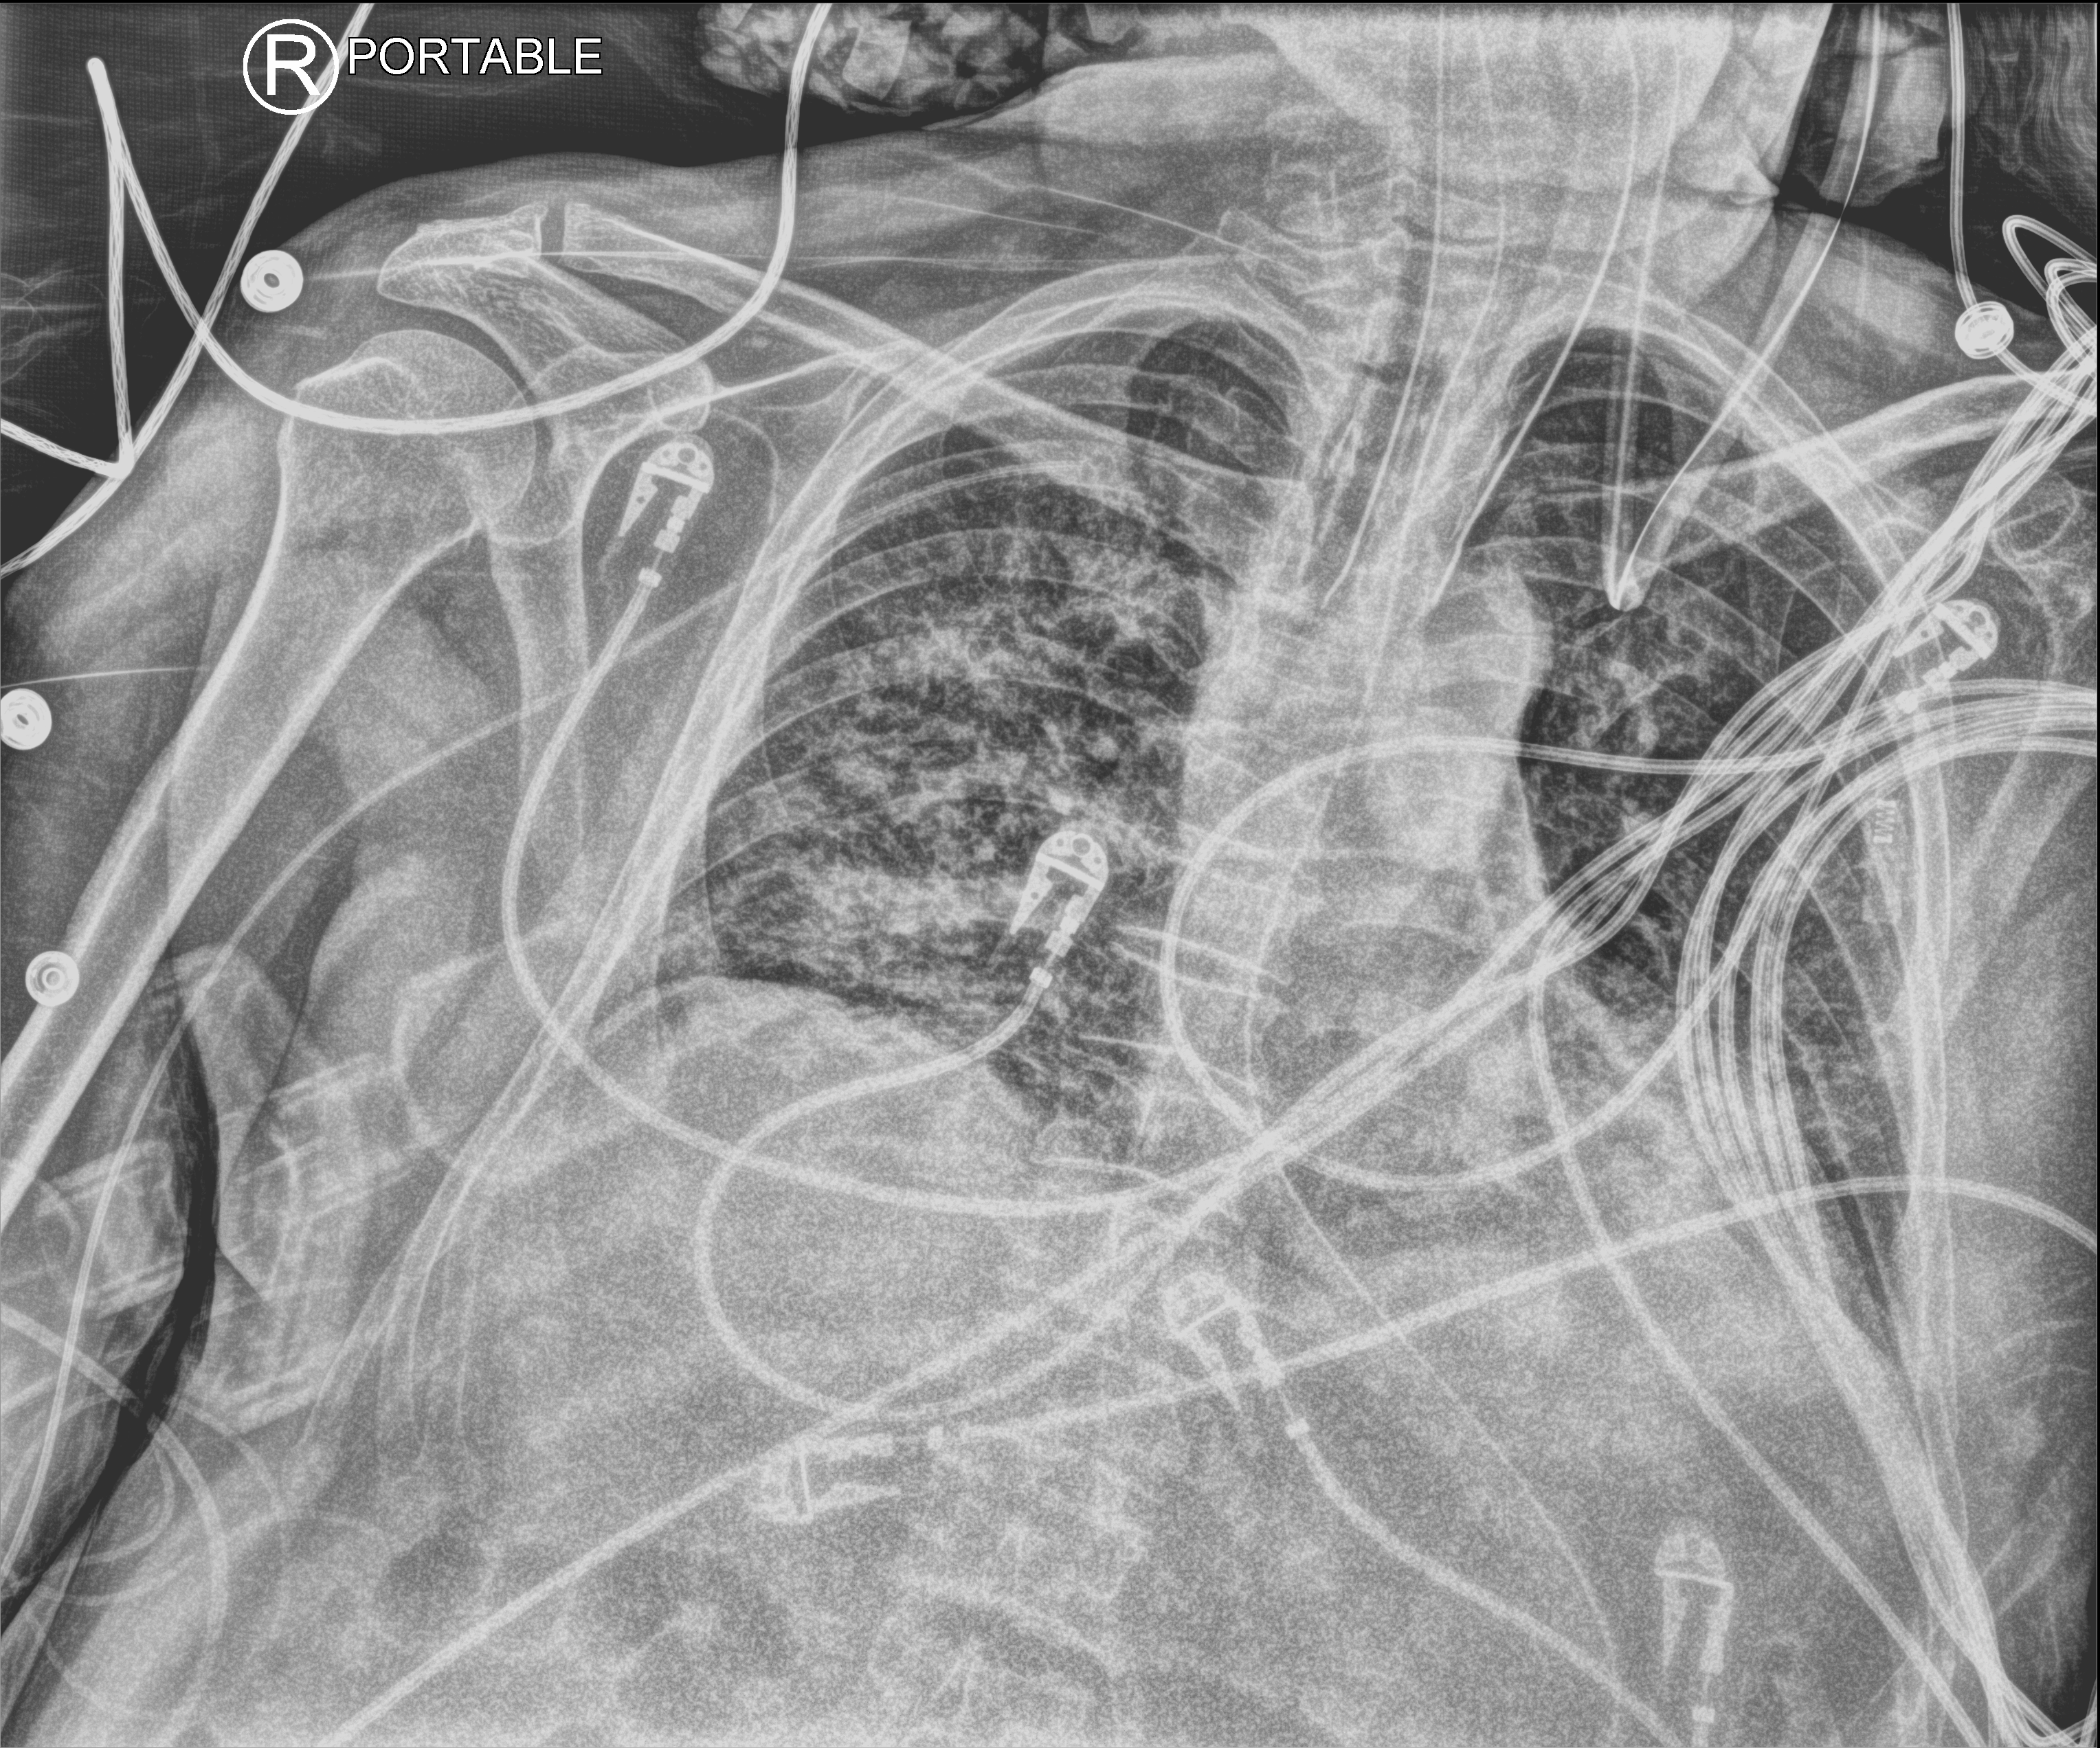
Chest X-ray (portable); anteroposterior (AP) projection. Male patient hospitalised with COVID-19, age 60–74 years.
Admission-level facts for this patient (not findings on this image; timing relative to this image not recorded):
- mechanically ventilated during this hospital stay: yes